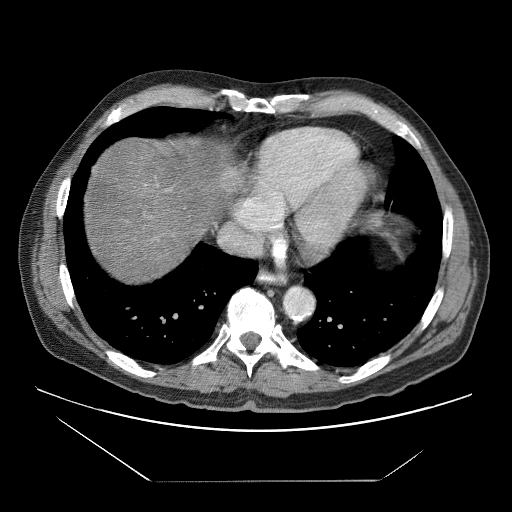
Contrast-enhanced abdominal CT (liver protocol), one axial slice; position 69 of 83 along the scan axis; reconstruction kernel STANDARD; soft-tissue window (W 400 / L 40 HU); 2.5 mm slice thickness; 512 × 512 image matrix. From the clinical record (not read from this slice): diagnosis: hepatocellular carcinoma (patient treated with transarterial chemoembolisation; whether this scan precedes or follows treatment is not stated here); TNM stage (as recorded): Stage-IVB; Child-Pugh class: B; tumour differentiation: poorly differentiated; tumour nodularity: uninodular.
Annotated regions visible in this slice (semi-automatically segmented with operator editing):
- liver parenchyma outside the tumour (the mass and vessels are separate outlines, so this box may not span the whole liver): box from (x=86, y=138) to (x=230, y=282) px
- mass: (x=218, y=164)–(x=244, y=193)
- liver vessels: (x=145, y=184)–(x=171, y=191)